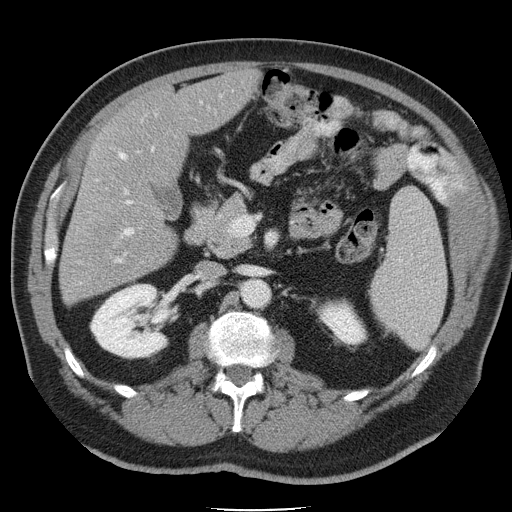
Contrast-enhanced abdominal CT, one axial slice. 120 kVp. Soft-tissue window (W 400 / L 40 HU). 5 mm slice thickness. 512 × 512 image matrix. Male patient, age 65 years. Case-level facts recorded for this patient, not image findings: diagnosis: colorectal cancer liver metastases, imaged before liver resection; multiple liver metastases: yes; largest metastasis: 4.9 cm; disease in both lobes: no.
Outlined on this slice (outlined manually by an expert reader):
- hepatic veins: box from (x=114, y=152) to (x=126, y=263) px
- liver: (x=60, y=72)–(x=258, y=303)
- planned liver remnant (the part of the liver to remain after resection): (x=96, y=71)–(x=259, y=183)
- portal vein (with intrahepatic branches): (x=124, y=148)–(x=154, y=235)